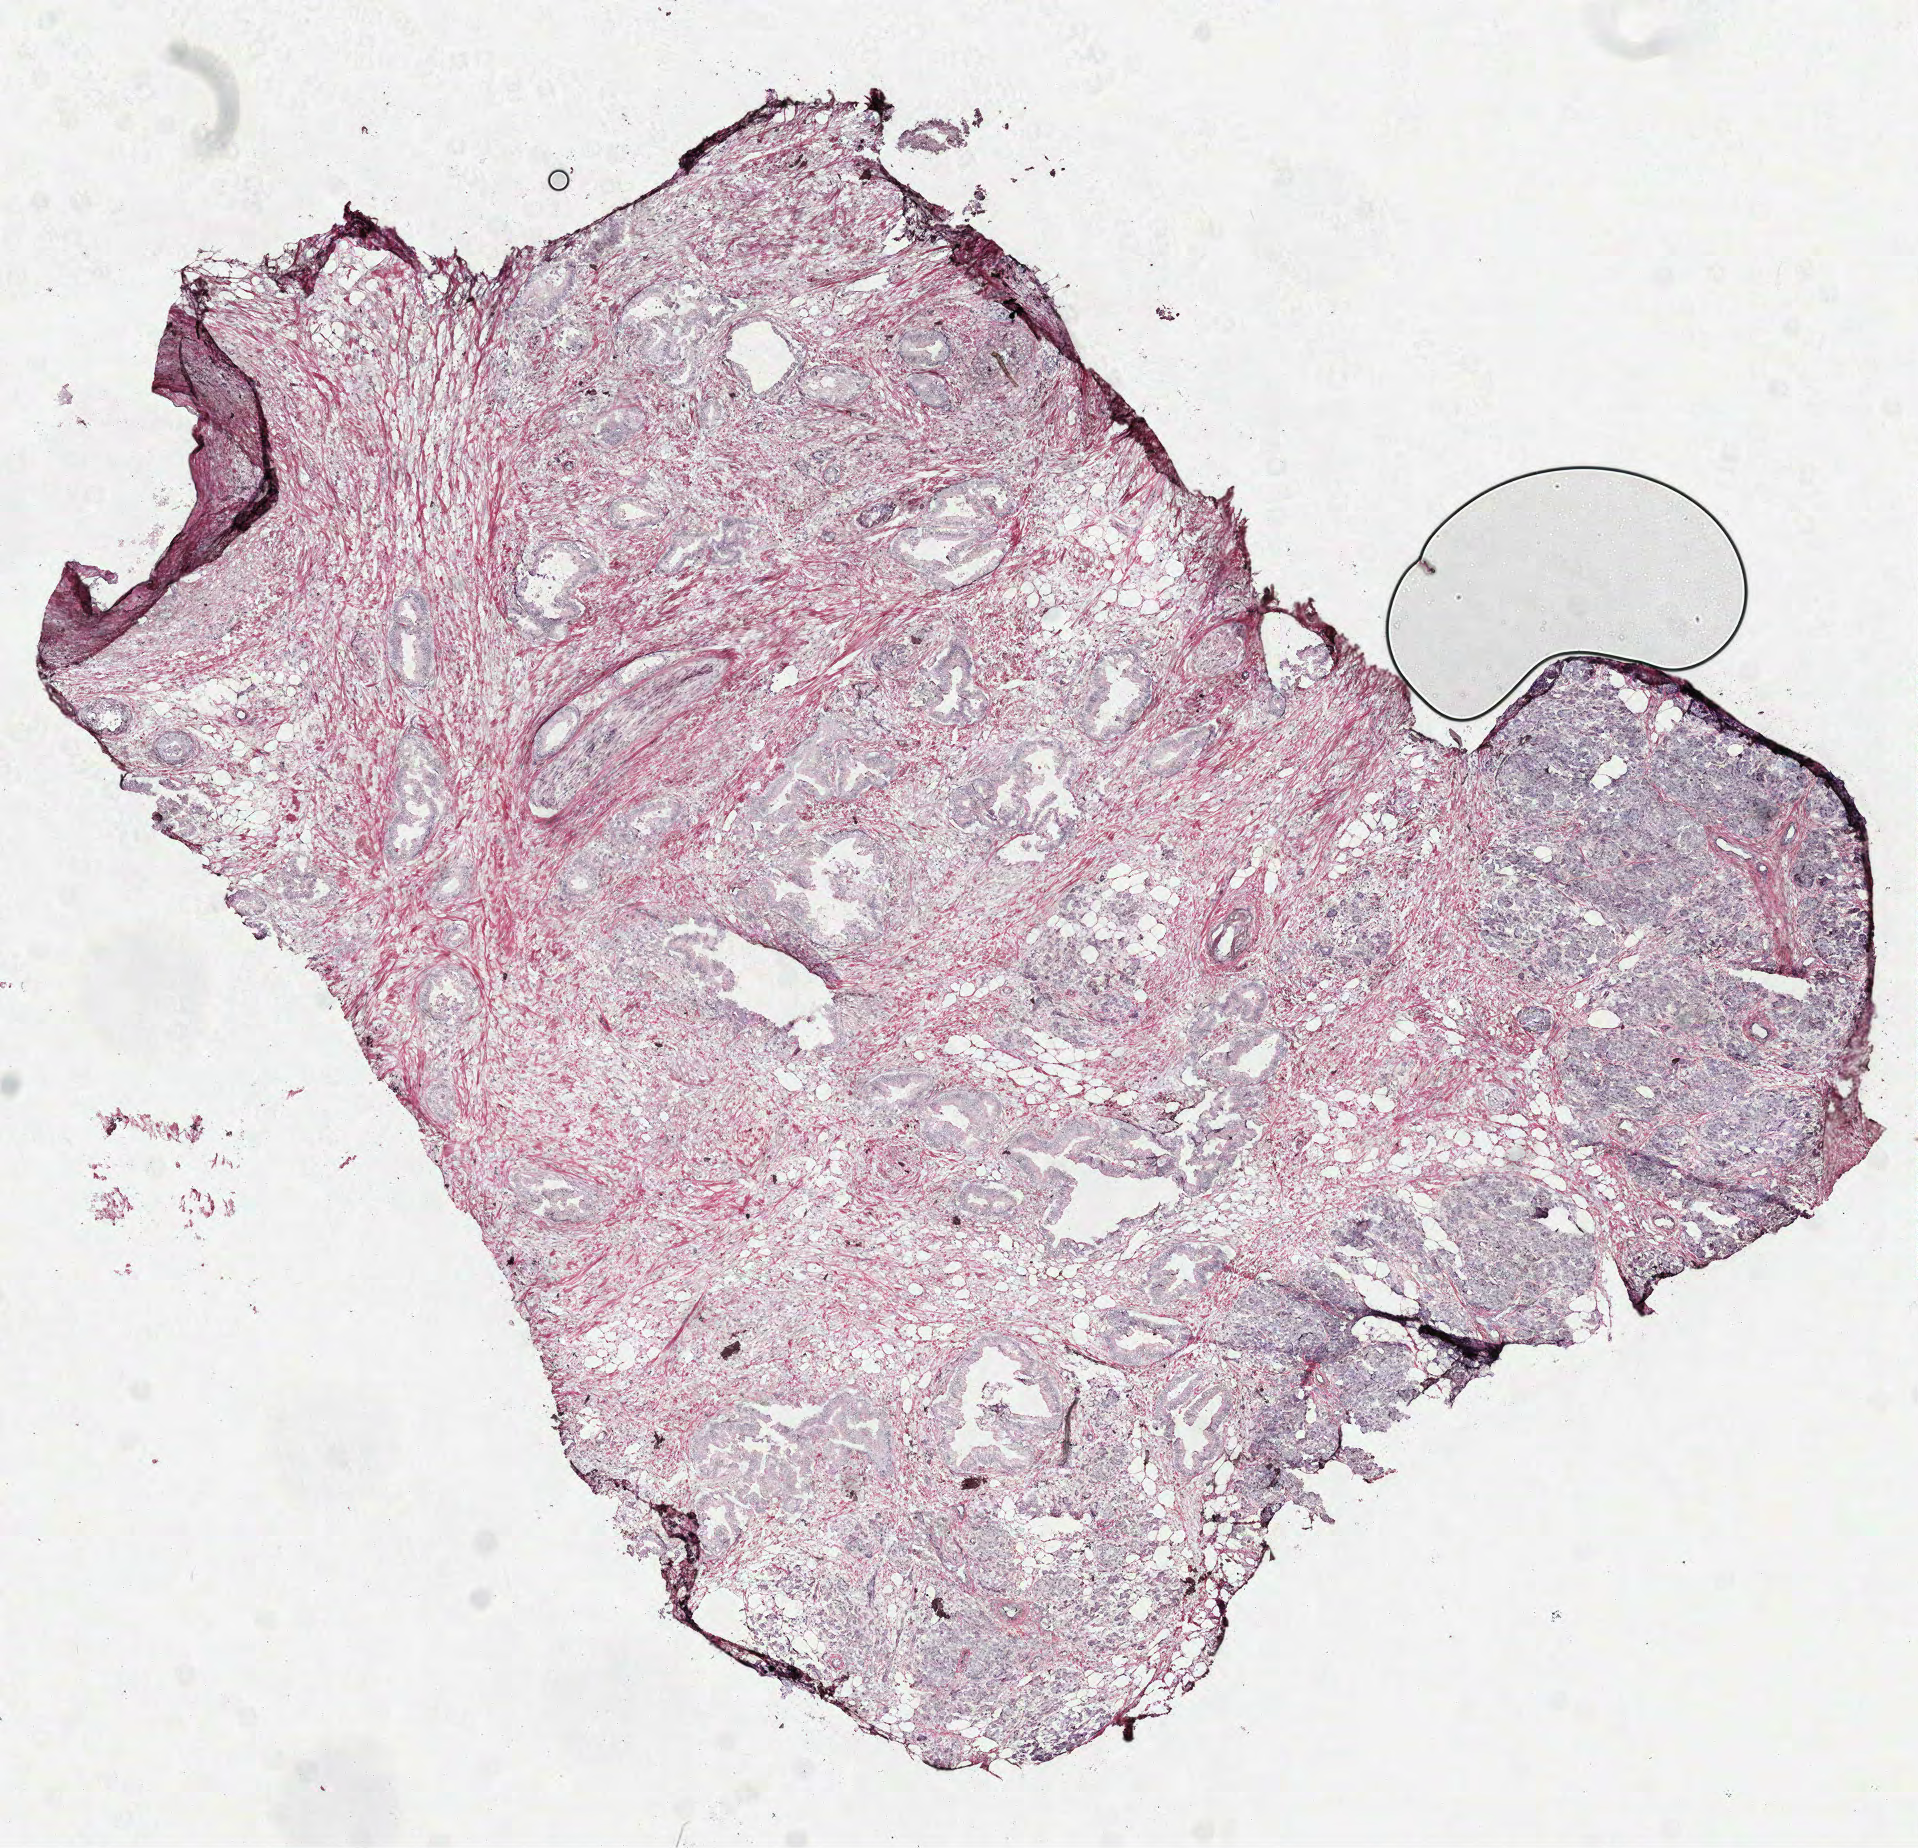
Digitized Hematoxylin and eosin (H&E) stained tissue section (whole slide), a low-resolution overview of the entire scanned area, about 7.7 x 7.5 mm (from a 40x scan). Frozen section. Pancreas, primary tumour sample. Patient: male, age at initial diagnosis 80 years. Histologic grade: G2 (moderately differentiated). Slide review estimates, as recorded: tumour cells 77%, tumour nuclei 65%, normal cells 6%, stromal cells 17%, necrosis 0%. Infiltration values recorded for this section: lymphocyte infiltration 2%, monocyte infiltration 0%, neutrophil infiltration 0%.
* histologic diagnosis: Infiltrating duct carcinoma, NOS (head of pancreas)
* AJCC pathologic stage: IIB (7th edition)